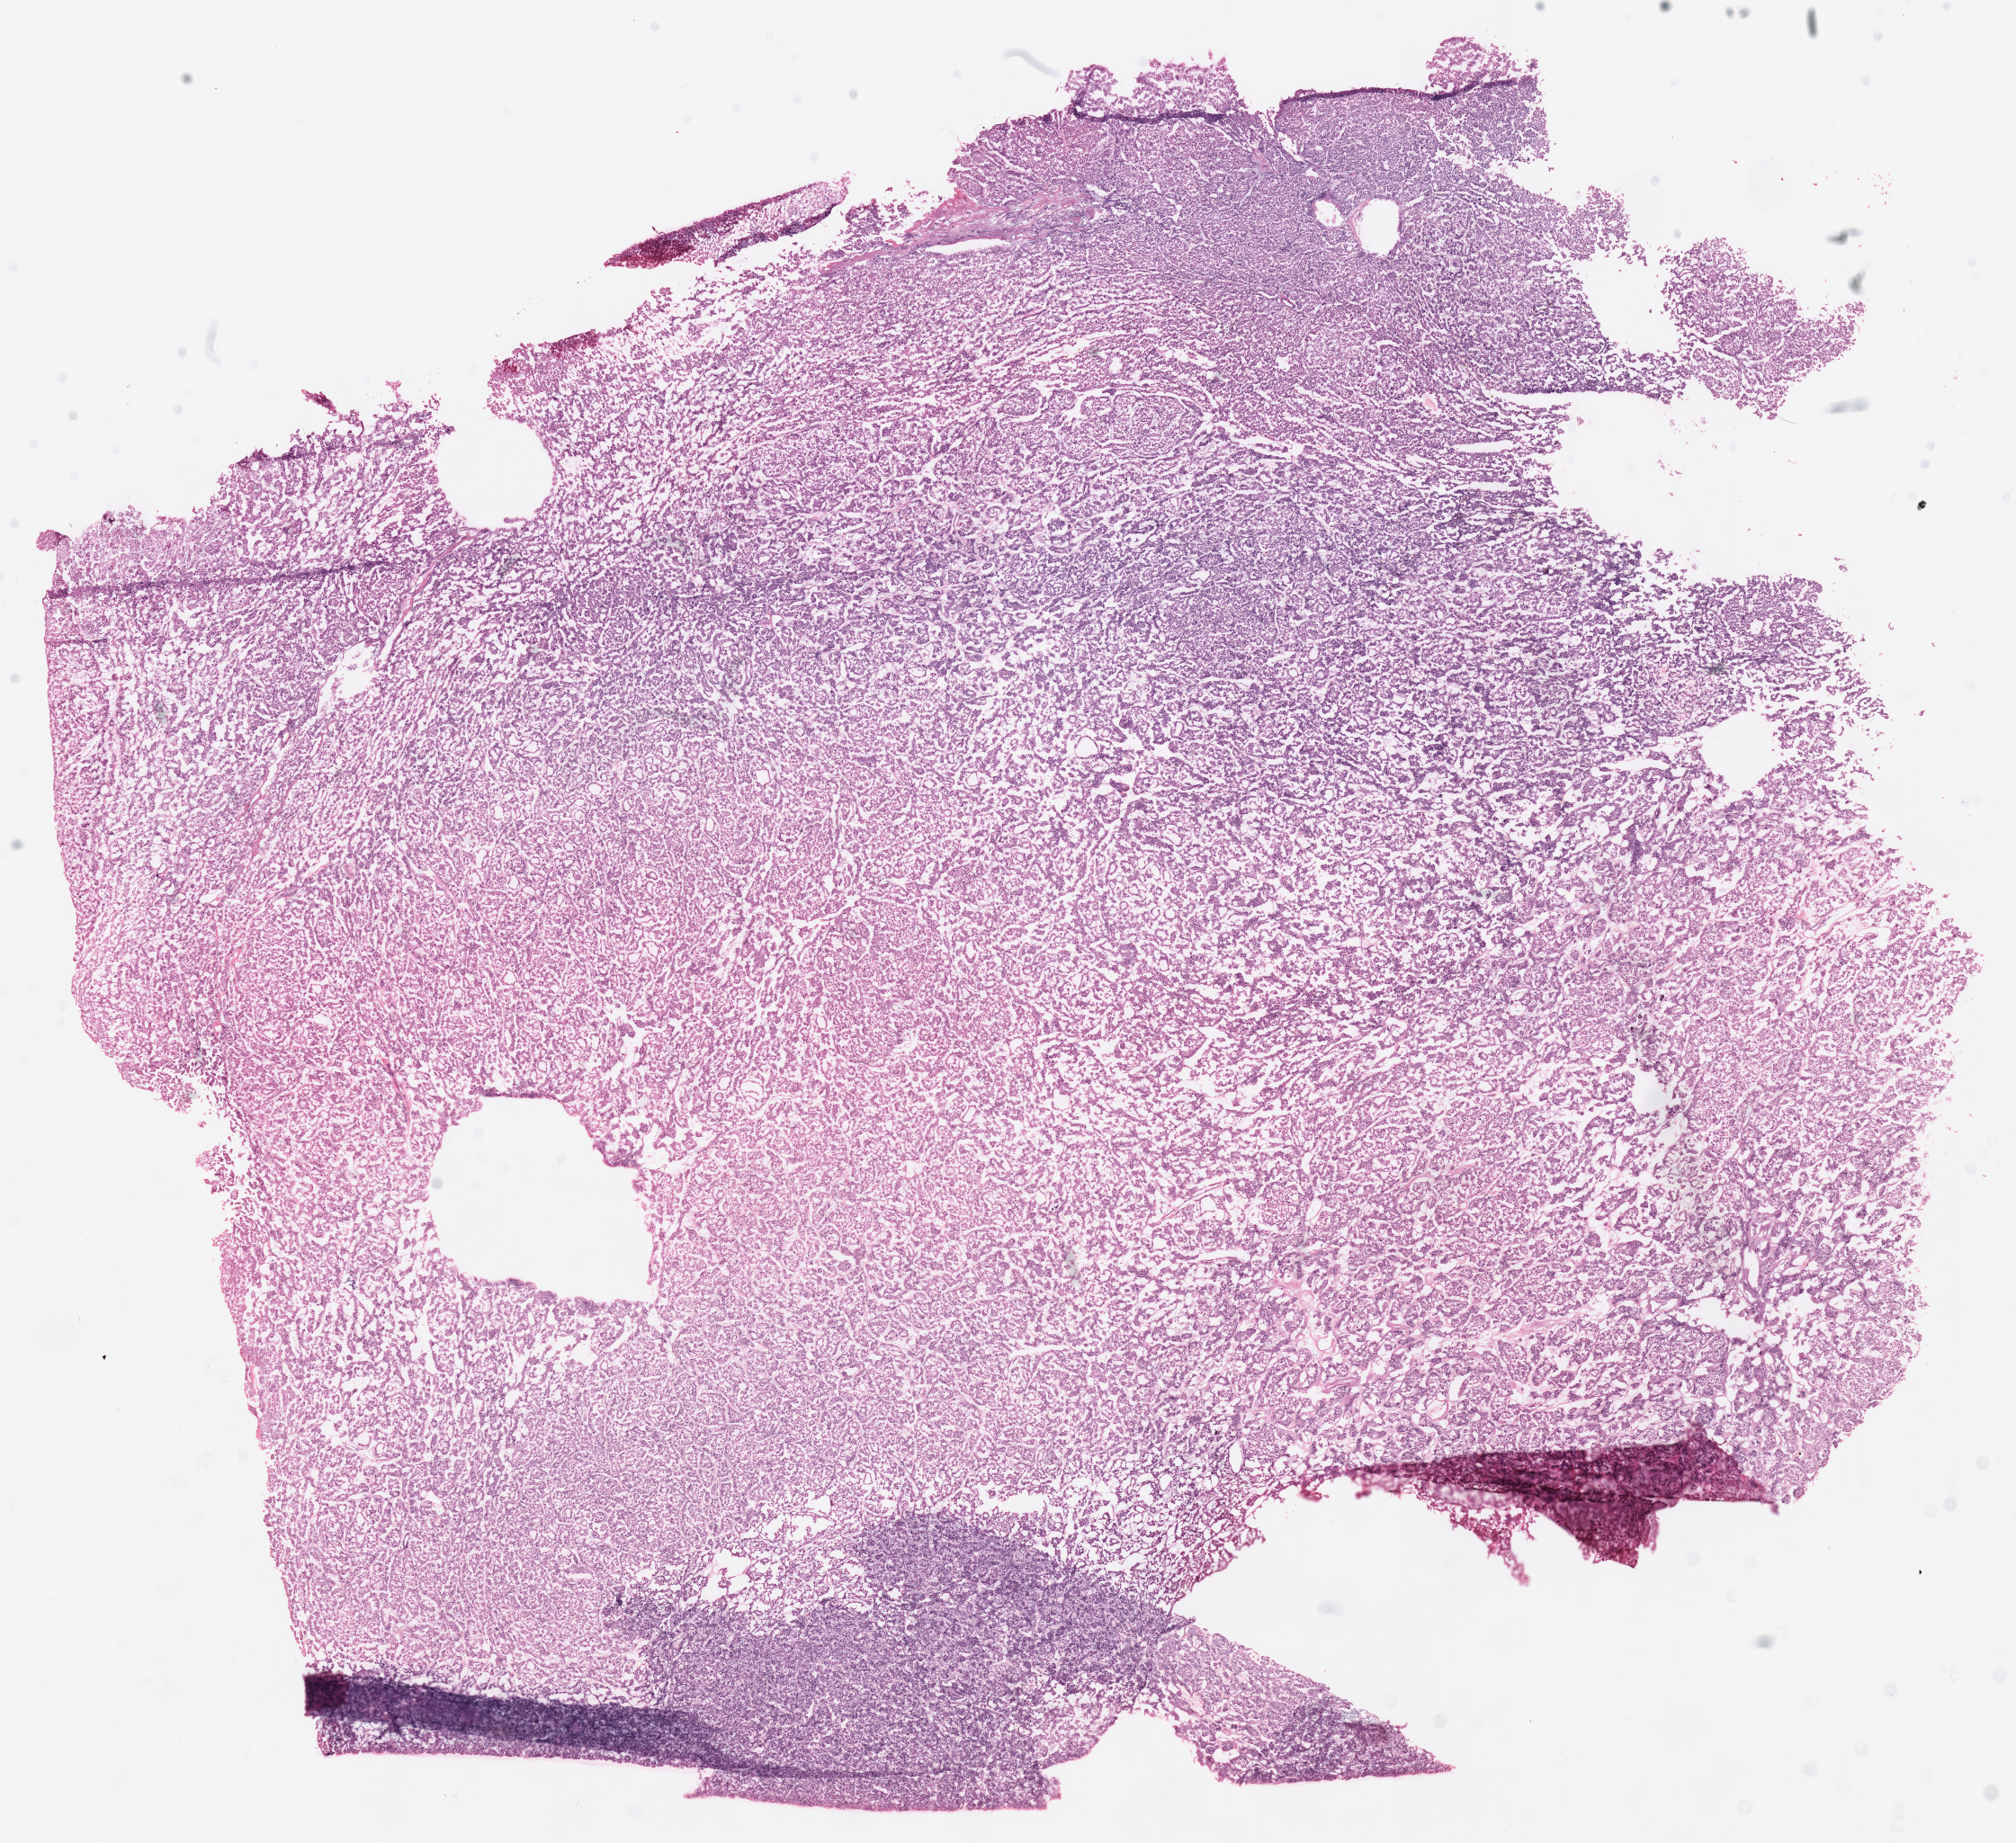
Whole-slide histology image, H&E-stained — shown as a low-resolution overview of the whole scanned area (about 17.6 x 16.1 mm, slide scanned at 40x), frozen section from the top of the tissue portion, kidney, primary tumour sample. Patient: male, age at initial diagnosis 44 years. Slide review estimates, as recorded: tumour cells 100%, tumour nuclei 95%, normal cells 0%, stromal cells 0%, necrosis 0%. Inflammatory infiltration, as recorded: lymphocyte infiltration 0%, monocyte infiltration 0%, neutrophil infiltration 0%.
Histologic diagnosis: Renal cell carcinoma, chromophobe type. AJCC pathologic stage: I (6th edition). TNM: T1b N0.